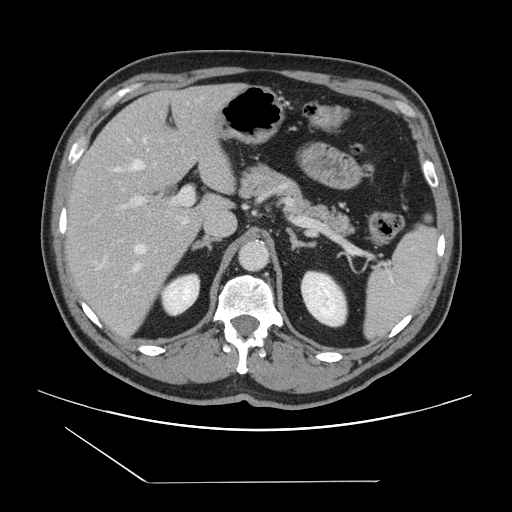
Contrast-enhanced abdominal CT, one axial slice. Slice 89 of 157 in the series (ordered by position). 120 kVp. Soft-tissue window (W 400 / L 40 HU). 2.5 mm slice thickness. 512 × 512 image matrix, field of view 407 × 407 mm. Male patient, age 61 years. Case-level facts recorded for this patient, not image findings: diagnosis: colorectal cancer liver metastases, imaged before liver resection; multiple liver metastases: yes; largest metastasis: 5.5 cm; chemotherapy before resection: no.
Annotated regions visible in this slice (manually delineated by an expert):
- hepatic veins: bounding box [x1, y1, x2, y2] px = [100, 139, 147, 270]
- liver: [66, 85, 241, 338]
- planned liver remnant (the part of the liver to remain after resection): [66, 84, 234, 221]
- portal vein (with intrahepatic branches): [100, 186, 194, 265]